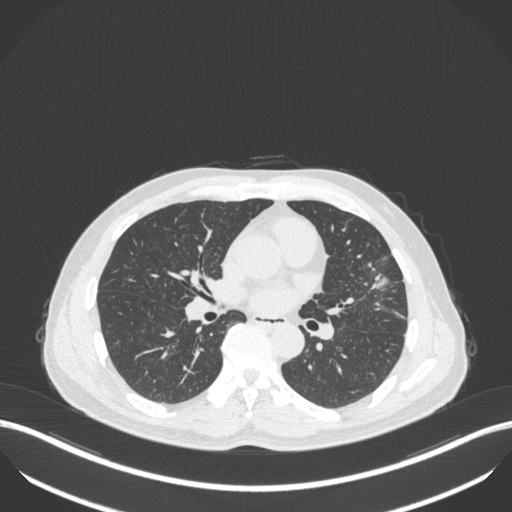
Chest CT, one axial slice. Slice 204 of 418 in the series (ordered by position). 120 kVp. Lung window (W 1500 / L -600 HU). 1 mm slice thickness. 512 × 512 image matrix, field of view 400 × 400 mm. Patient: male, 55 years. From the clinical record (not read from this slice): clinical TNM (as recorded): T1c N0 M0.
Structures marked on this image (bounding box drawn by a radiologist):
- lung tumour (recorded histology: adenocarcinoma): bounding box (x1, y1, x2, y2) in pixels: (363, 268, 394, 299)